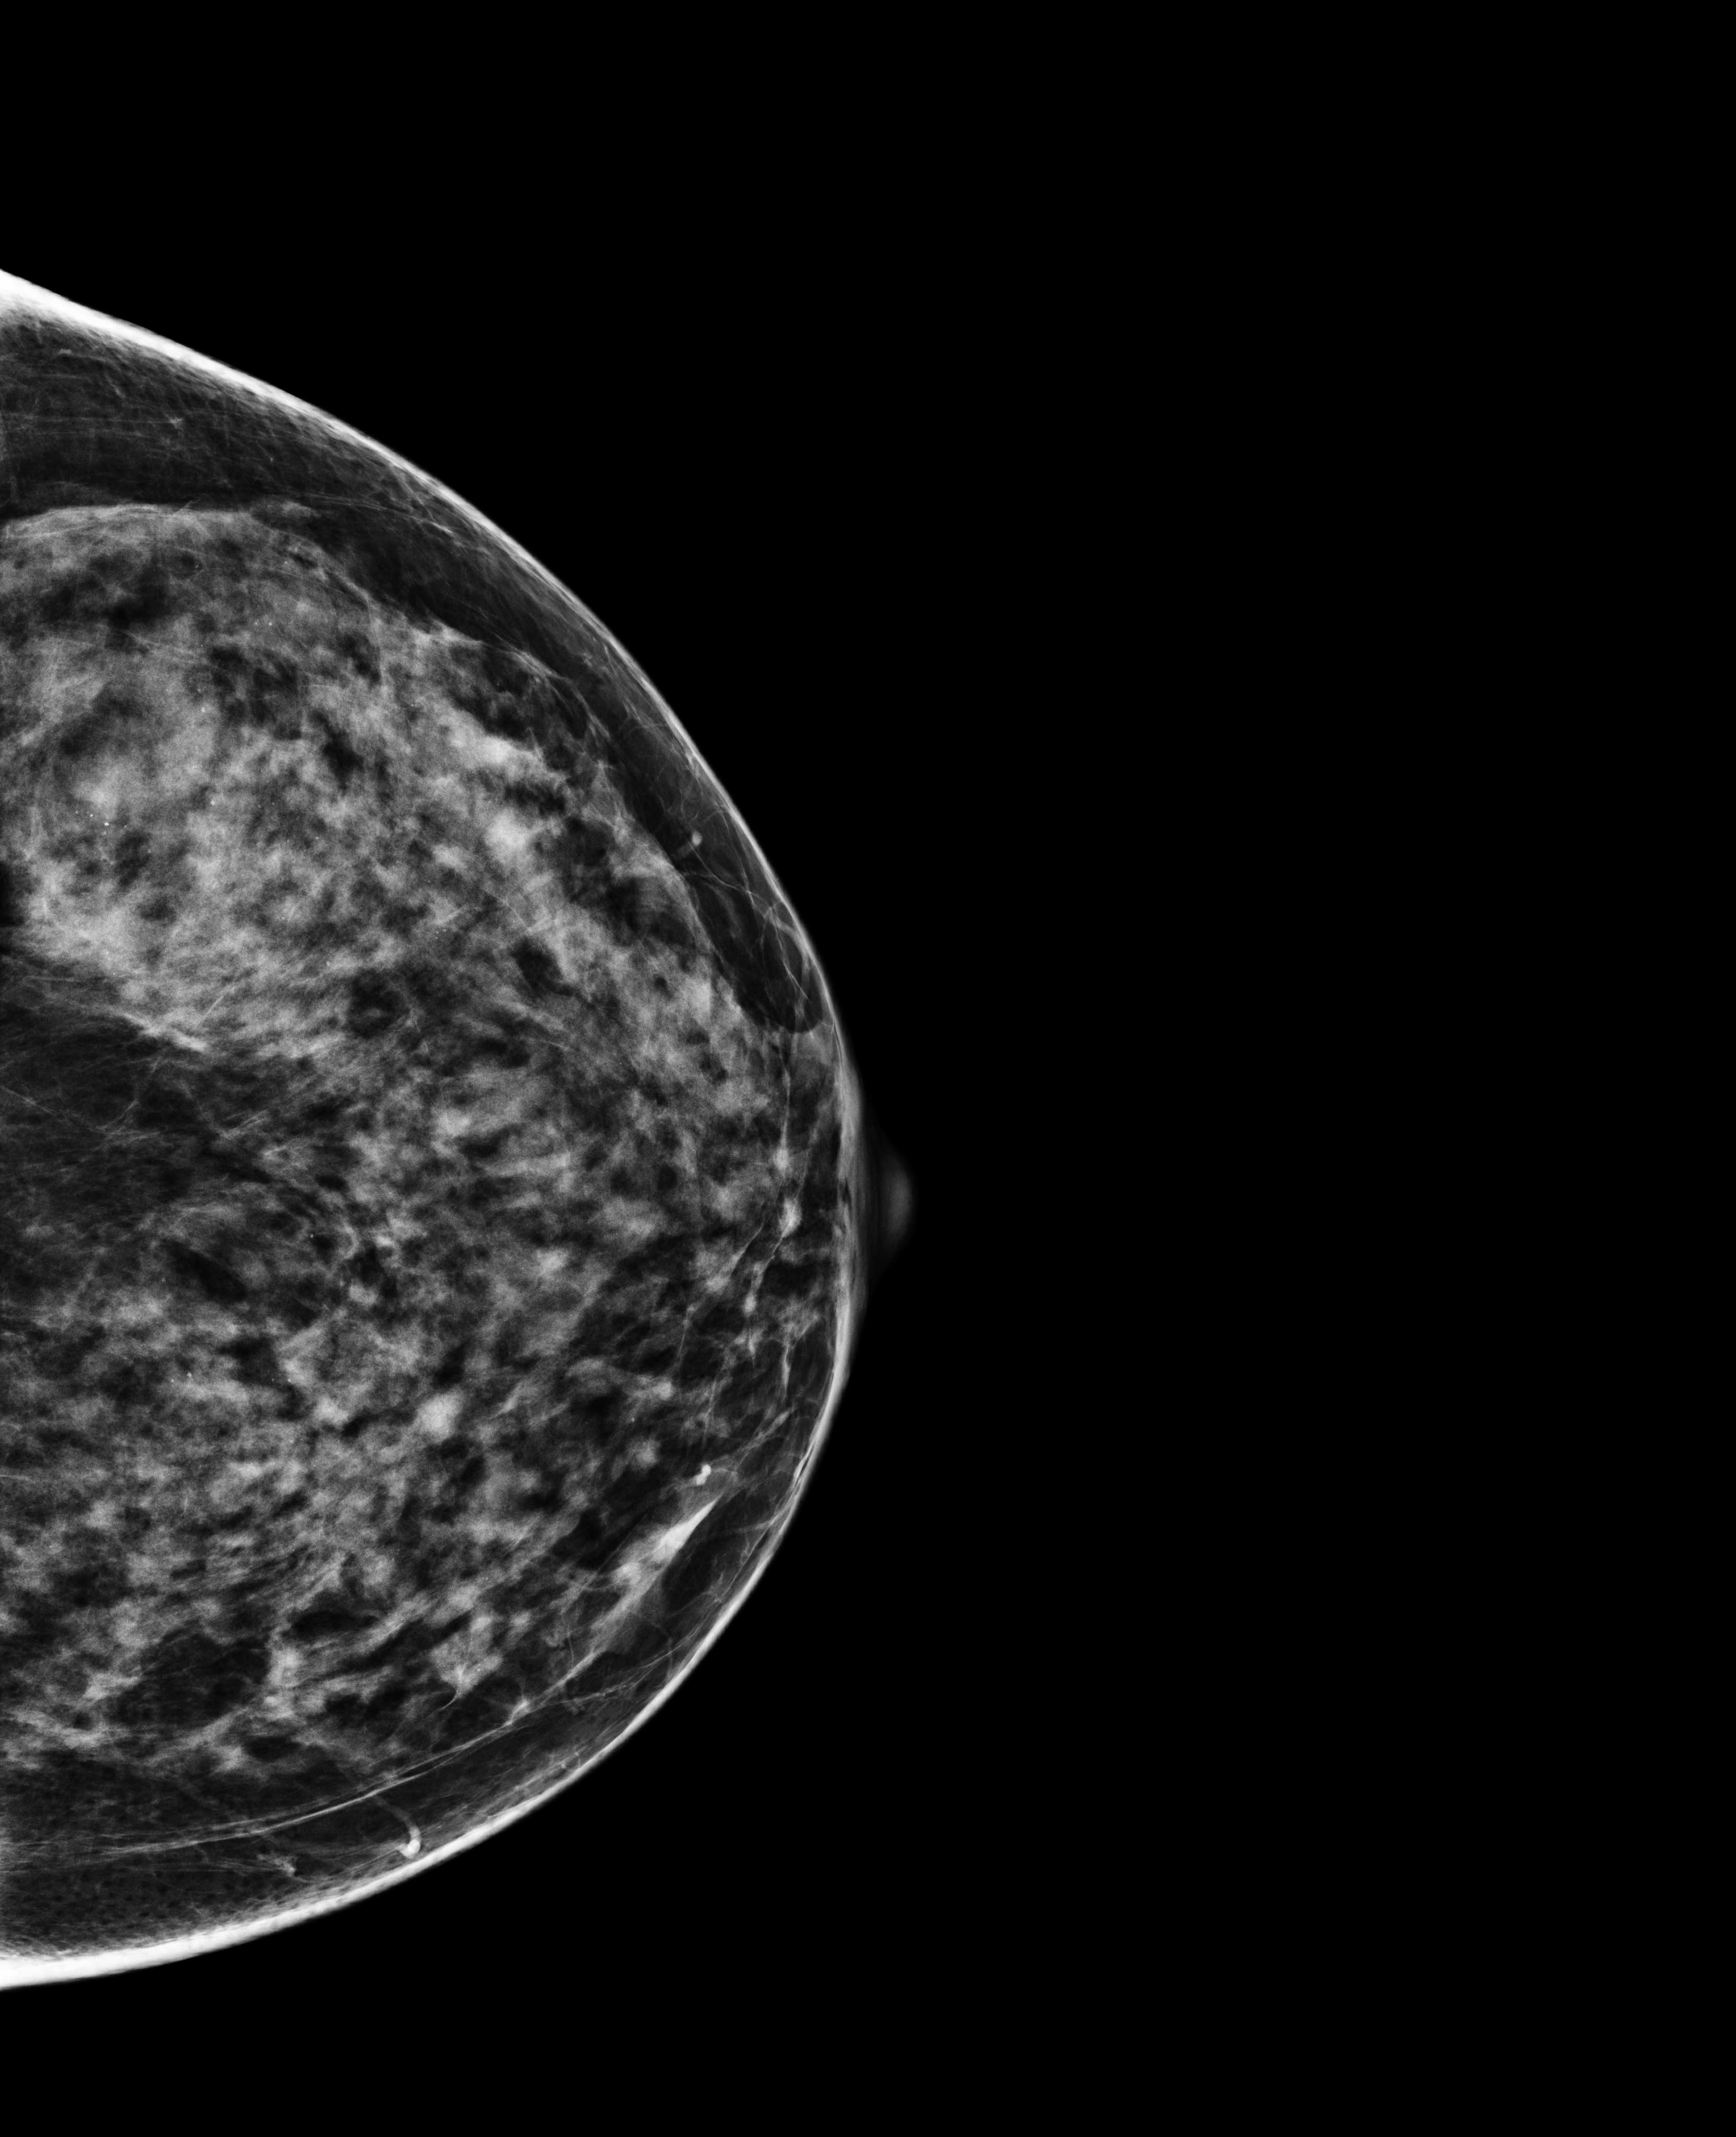
Annual screening mammography examination. Patient aged 51 years (female).
Image type: full-field digital mammogram. Breast: left. Projection: CC view. BI-RADS breast density category at the screening exam (both breasts, scale 1–4): 3. Final BI-RADS category for the screening round (tomosynthesis exam, both breasts): category 1. Recall: no recall after this screen.